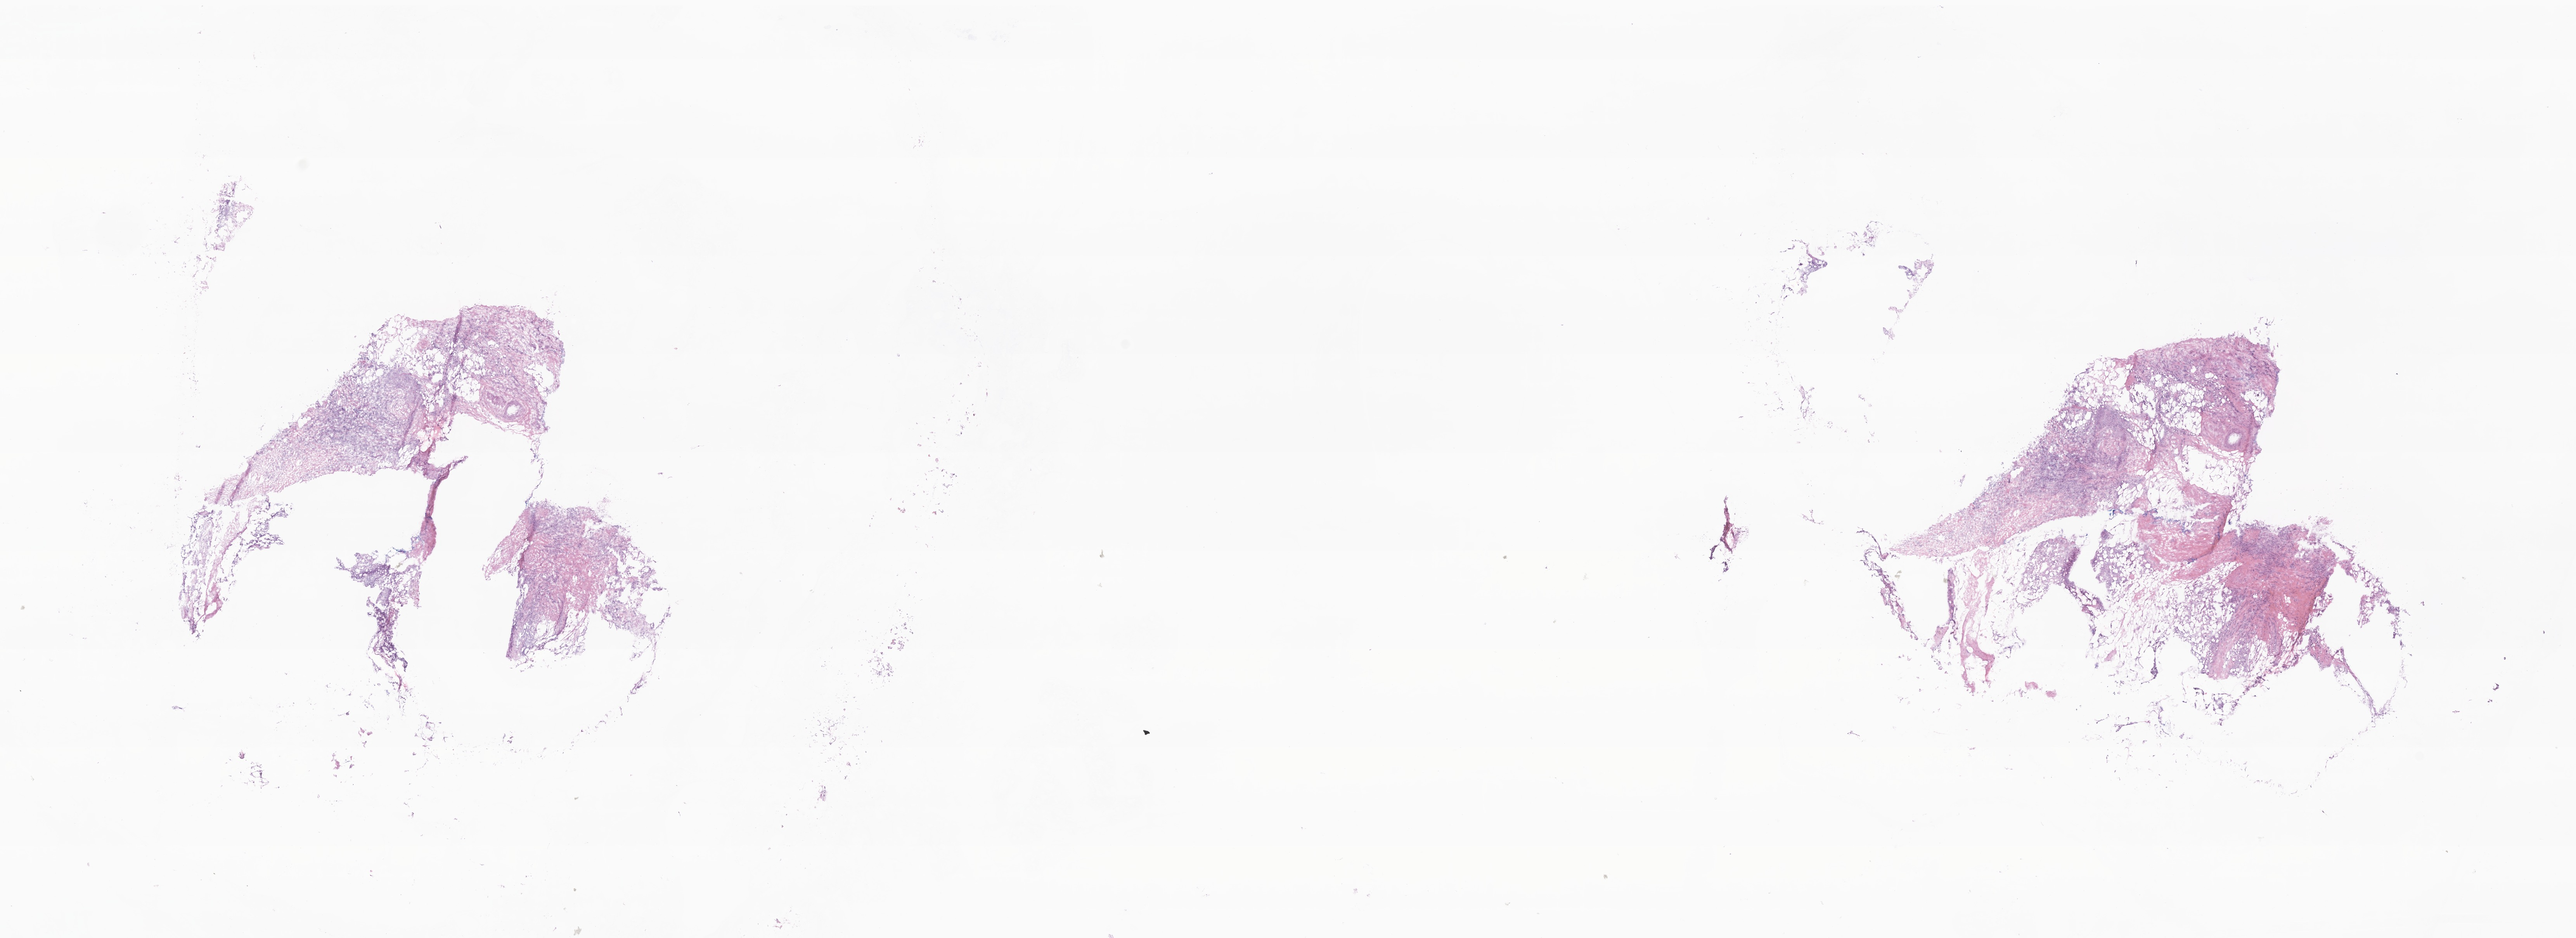
Haematoxylin and eosin whole-slide image — whole scanned area (about 28.0 x 10.2 mm) shown as a low-resolution overview; frozen section (tissue freezing medium); primary tumor; site: breast. Female patient; age at initial diagnosis 62 years. Composition of this section per pathologist review: tumor cells 95%, tumor nuclei 75%, stromal cells 0%, necrosis 0%, normal cells 5%. Inflammatory infiltration, as recorded: lymphocyte infiltration 0%, monocyte infiltration 0%, neutrophil infiltration 0%.
Diagnosis: Lobular carcinoma, NOS.